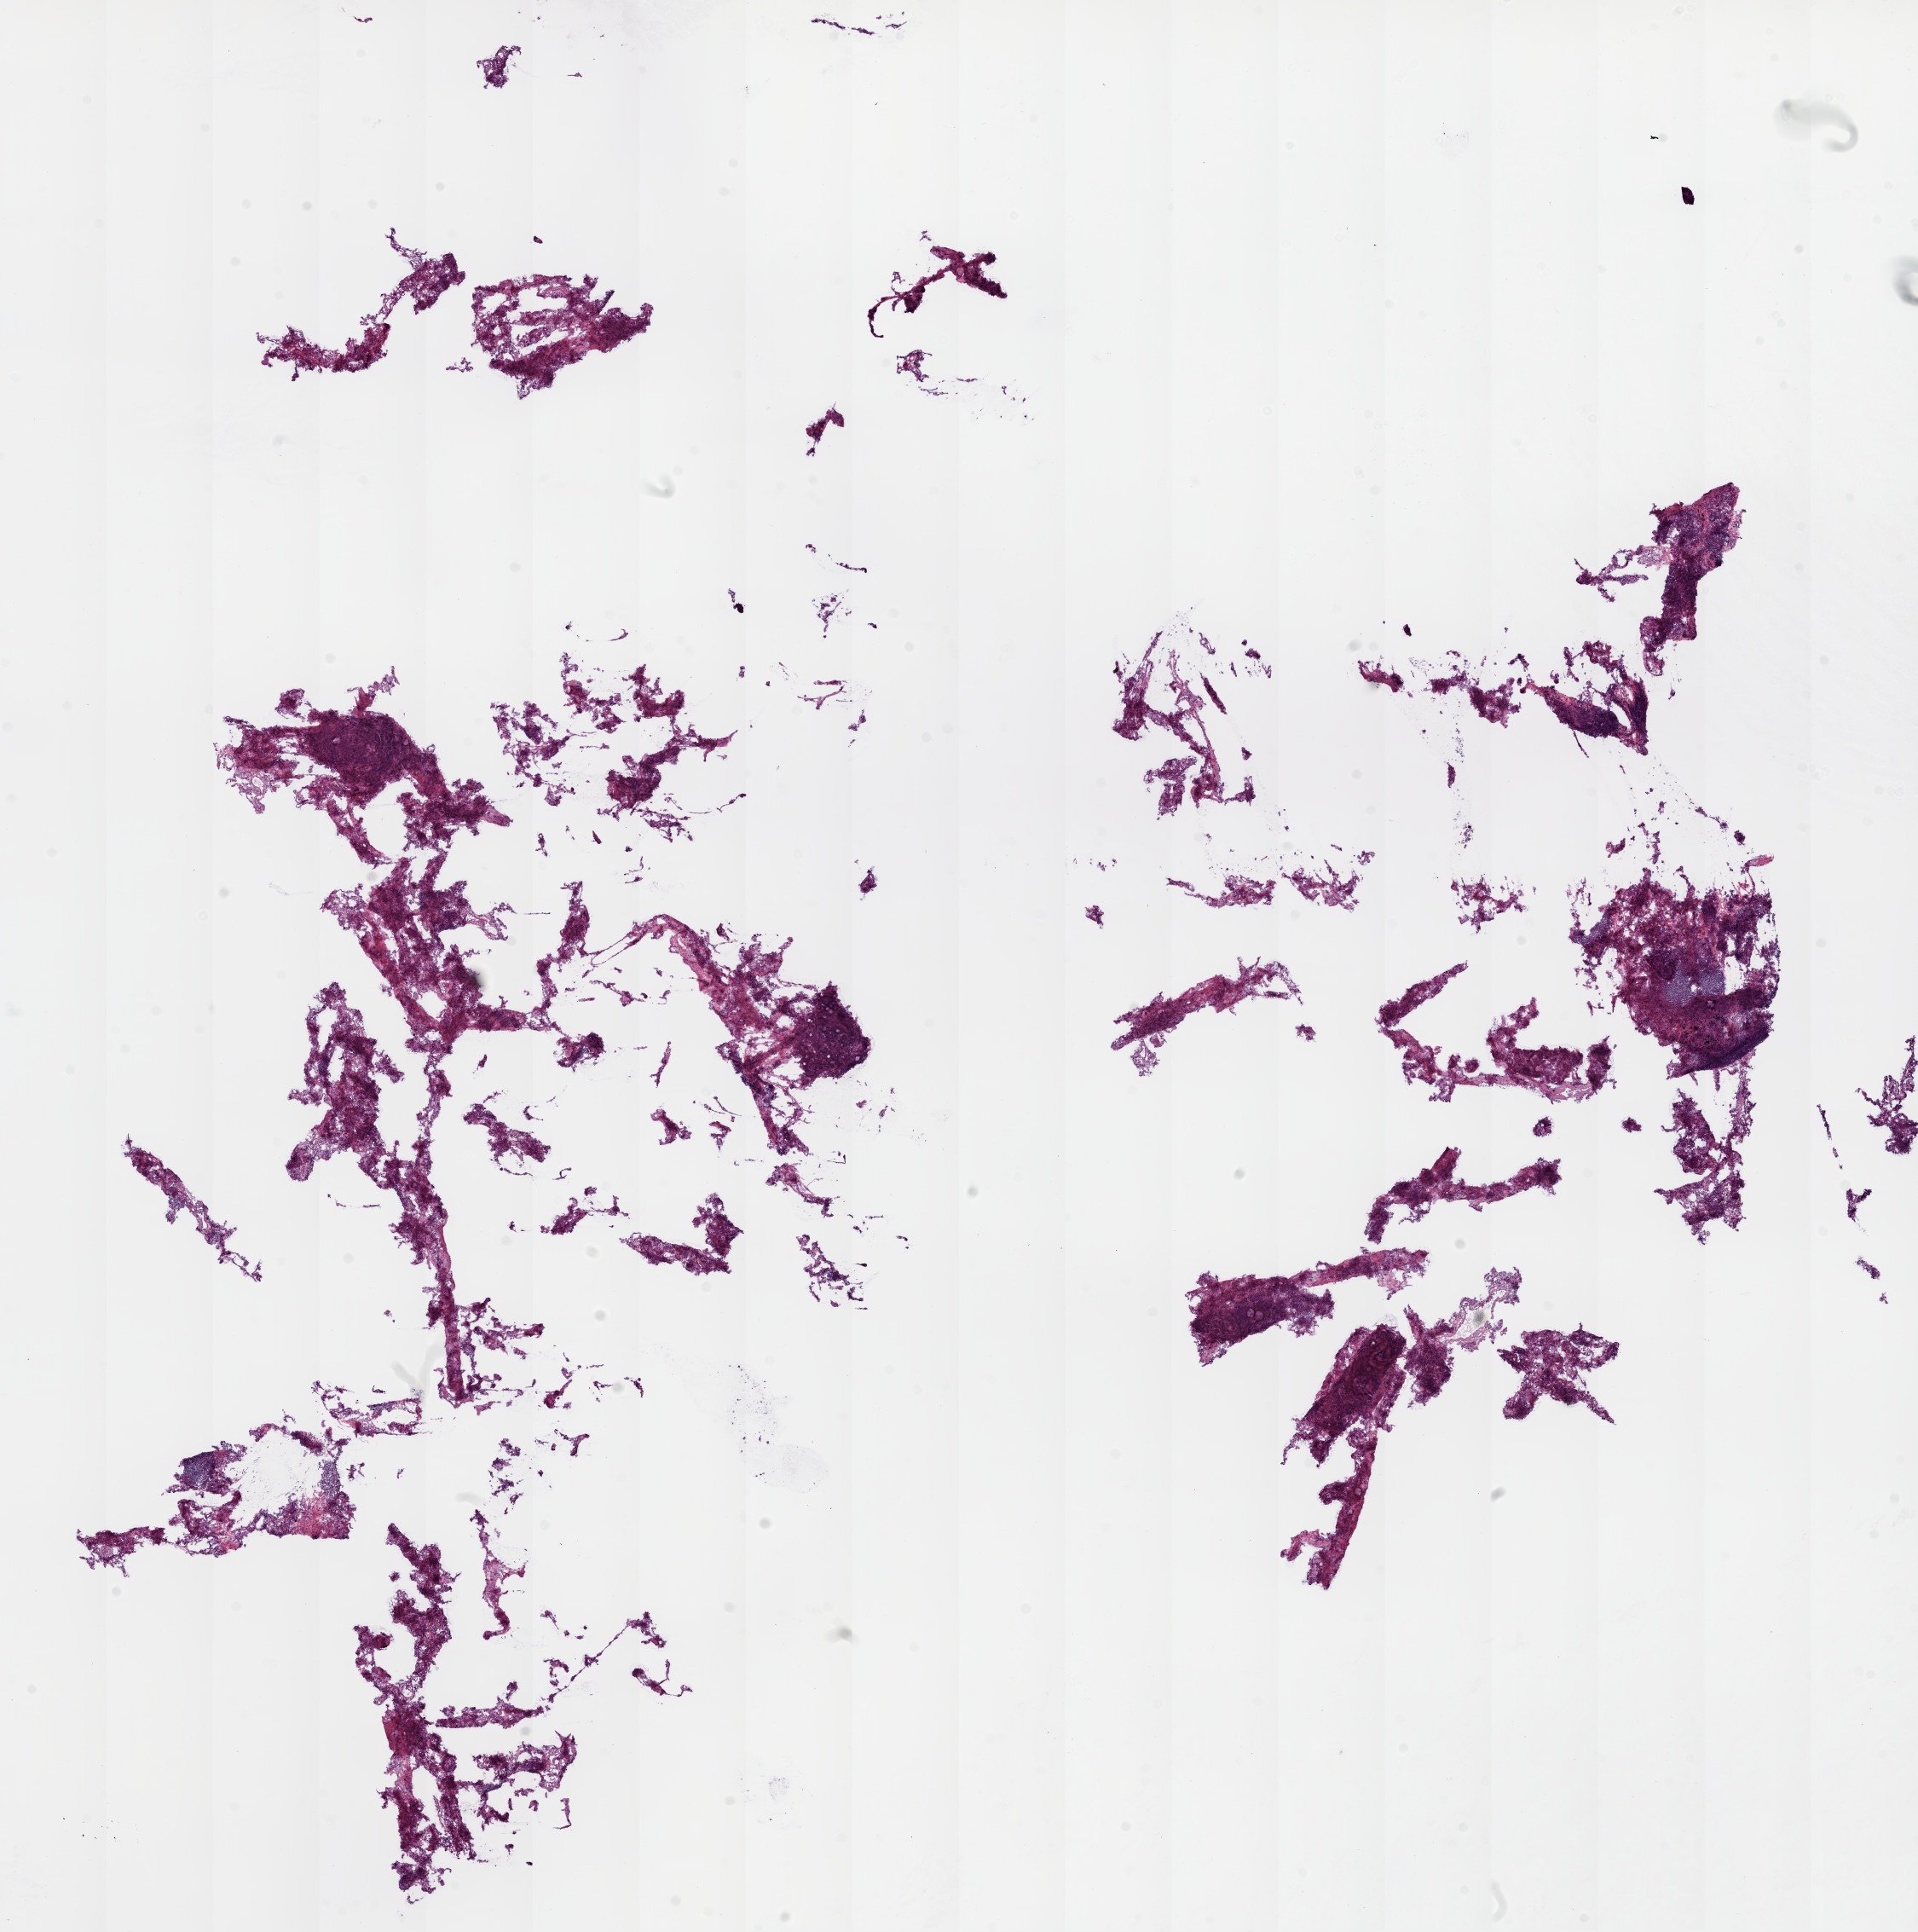
Digitized H&E tissue section (whole slide) — a low-resolution overview of the entire scanned area, about 18.1 x 18.2 mm; frozen section from the top of the tissue portion; solid tissue normal (non-tumour tissue) sample from the lung. Patient: female, age at initial diagnosis 74 years.
This section: solid tissue normal (non-tumour) sample from the same patient. Patient diagnosis: Adenocarcinoma, NOS (upper lobe, lung).